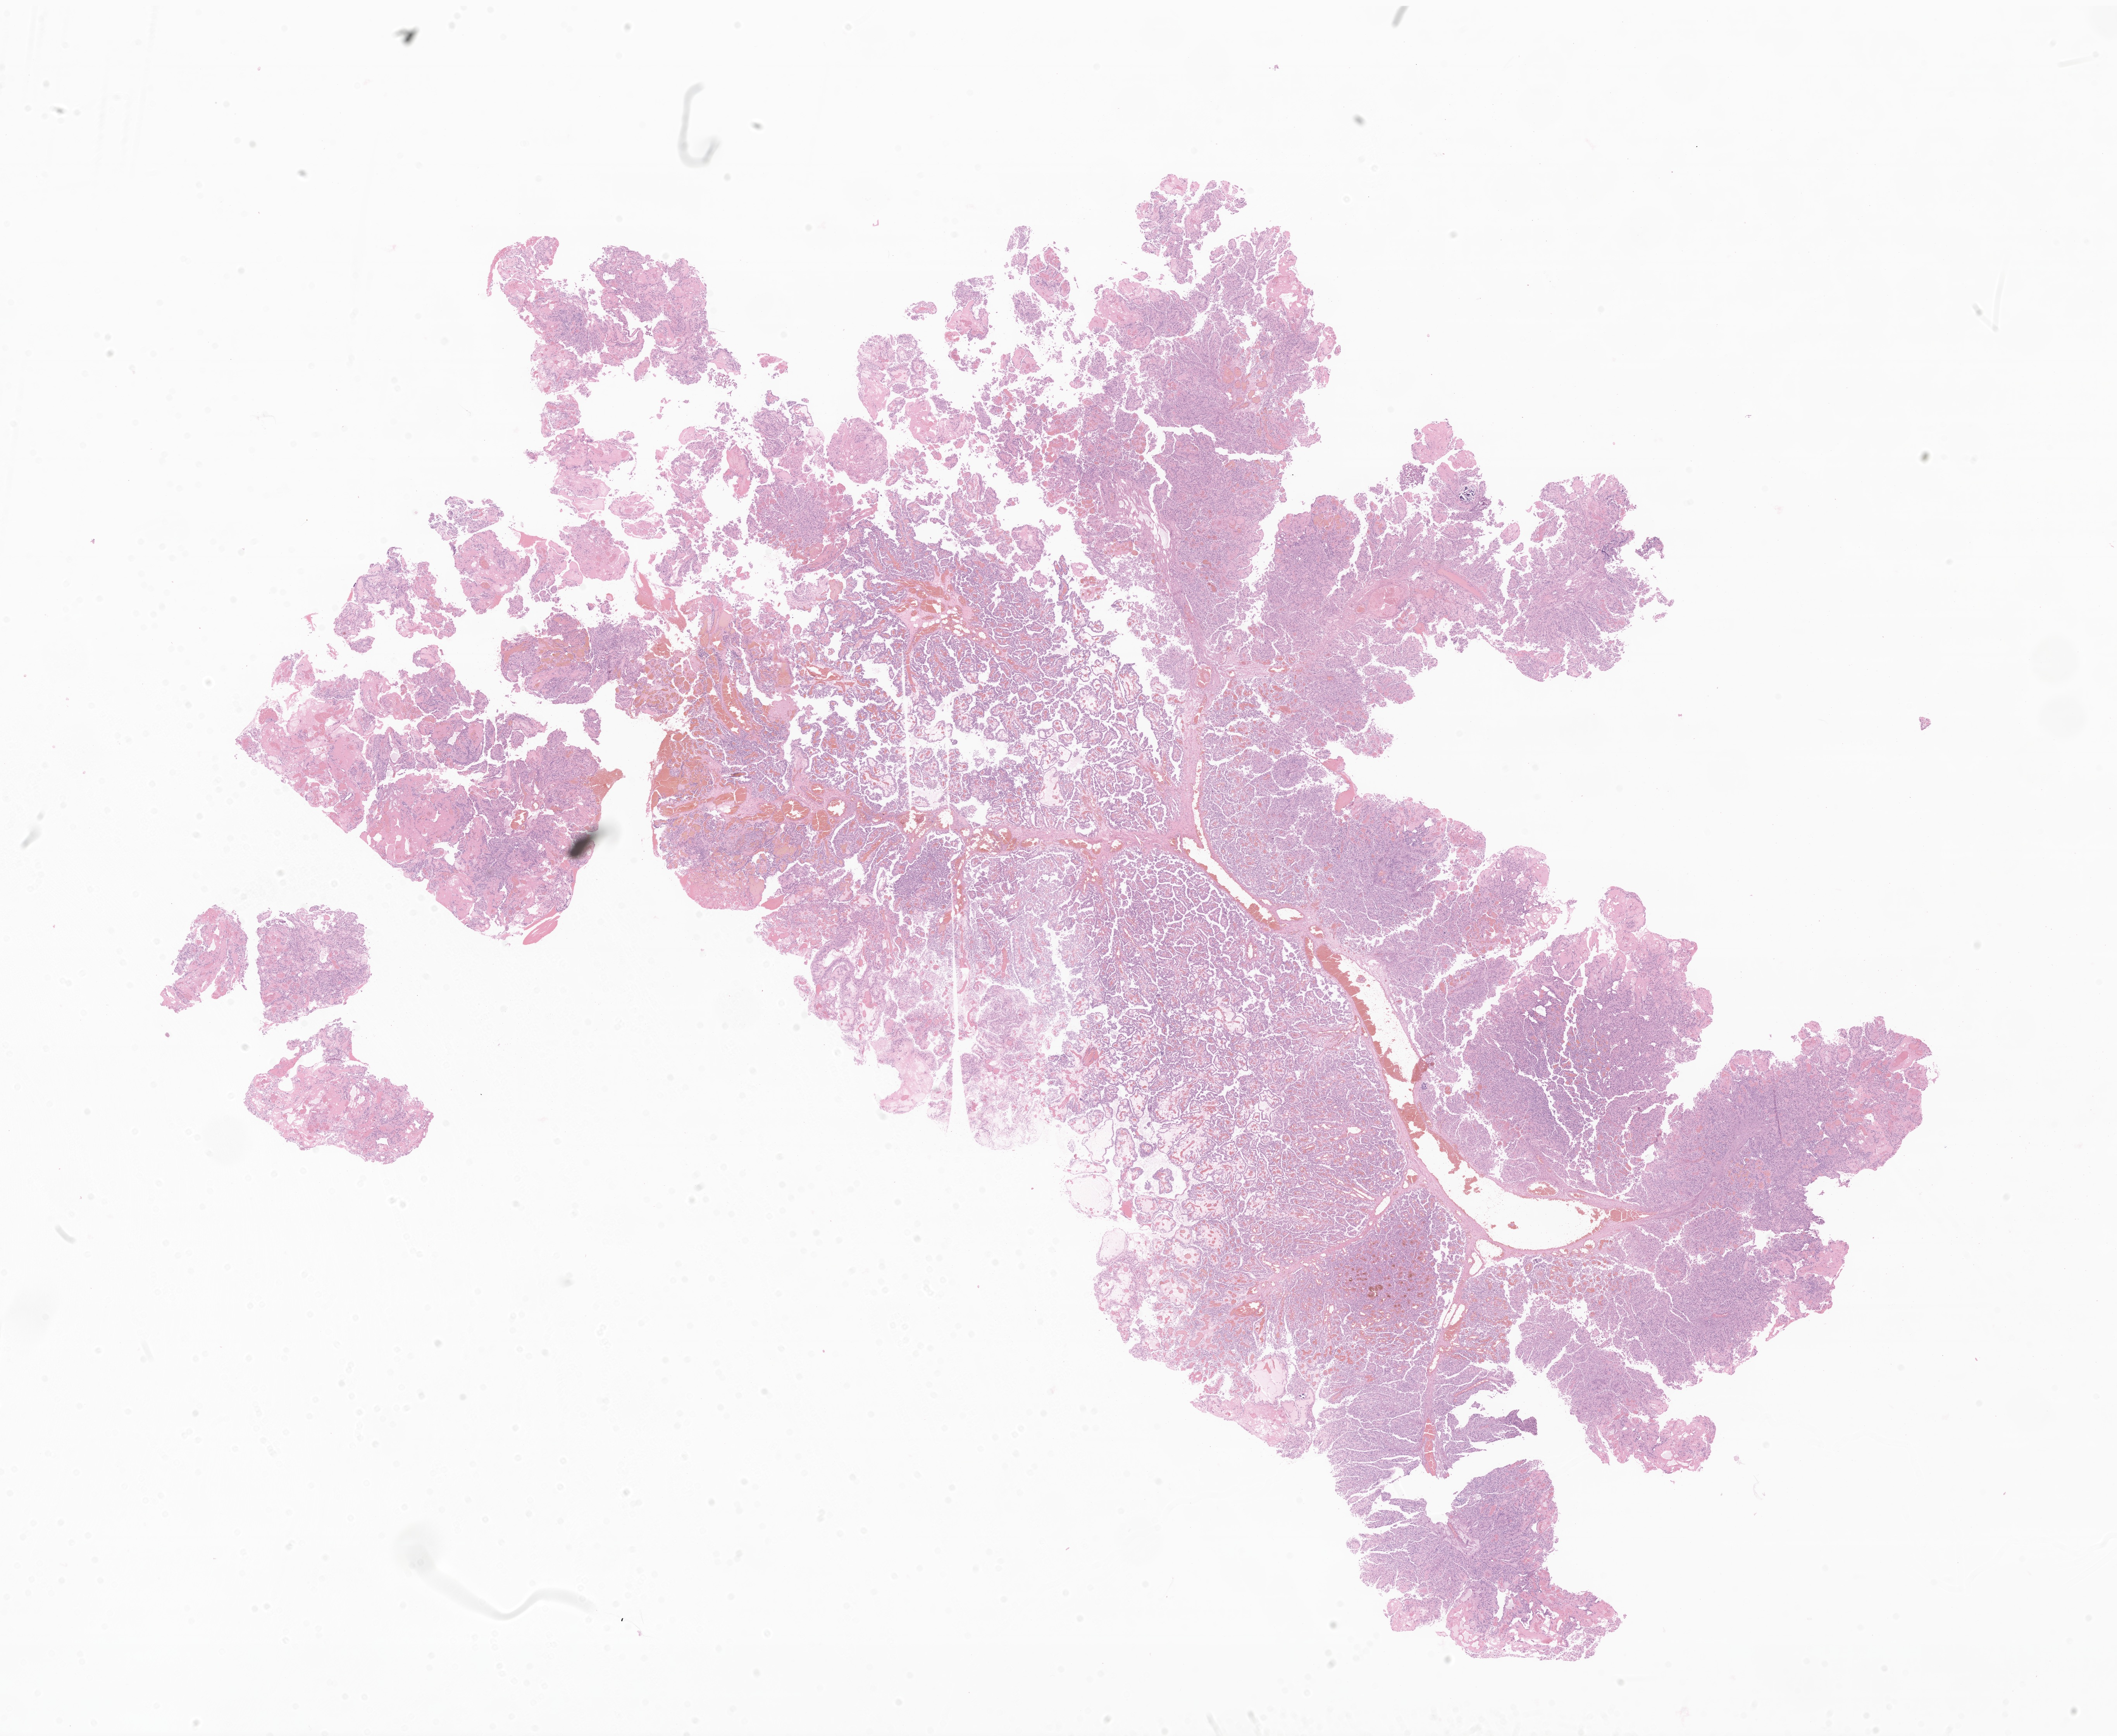
Hematoxylin and eosin (H&E) whole-slide image of tumor tissue from the brain — a low-resolution overview of the entire scanned area, about 23.0 x 18.9 mm. Formalin-fixed, paraffin-embedded (FFPE) tissue. Male patient, age 266 days.
Diagnosis: Choroid plexus papilloma, NOS.